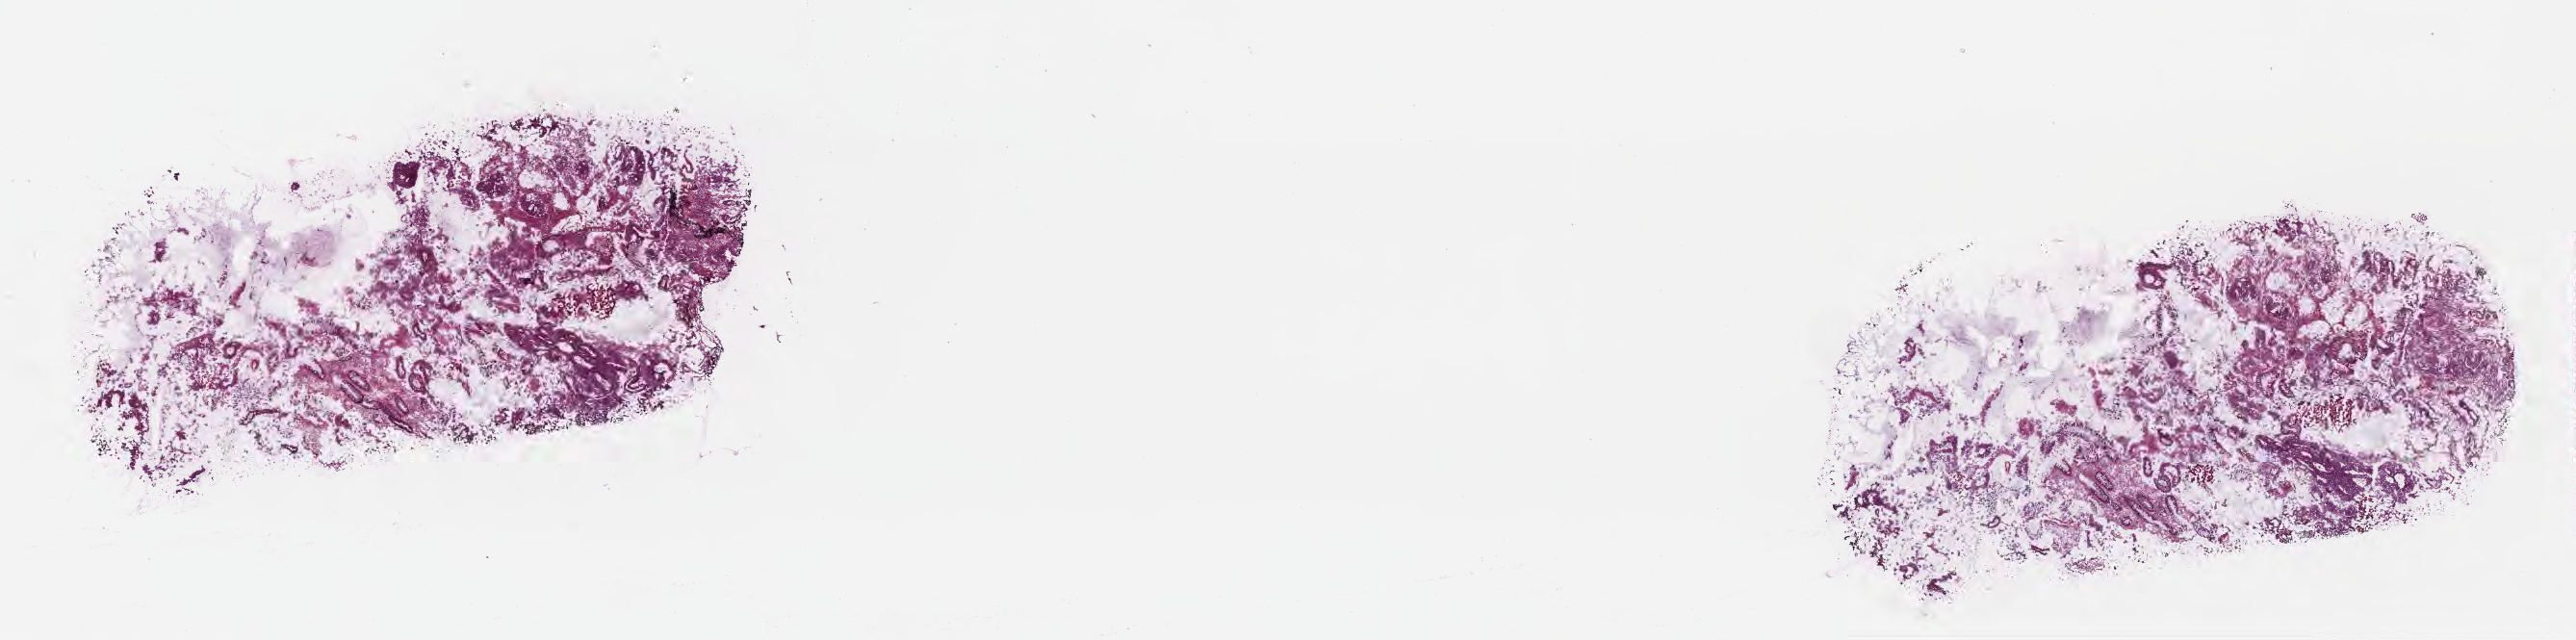
Whole-slide image, haematoxylin and eosin stain, whole scanned area (about 21.6 x 5.4 mm) shown as a low-resolution overview; frozen section; specimen: primary tumor; site: sigmoid colon. Male patient; age at initial diagnosis 54 years. Tumor grade: G2 (moderately differentiated). Composition of this section per pathologist review: tumor cells 70%, tumor nuclei 70%, stromal cells 23%, necrosis 2%, normal cells 5%. Infiltration values recorded for this section: lymphocyte infiltration 6%, monocyte infiltration 4%, neutrophil infiltration 8%.
AJCC pathologic stage: Stage IIIB. Section: bottom of the tissue portion. Diagnosis: Adenocarcinoma, NOS.